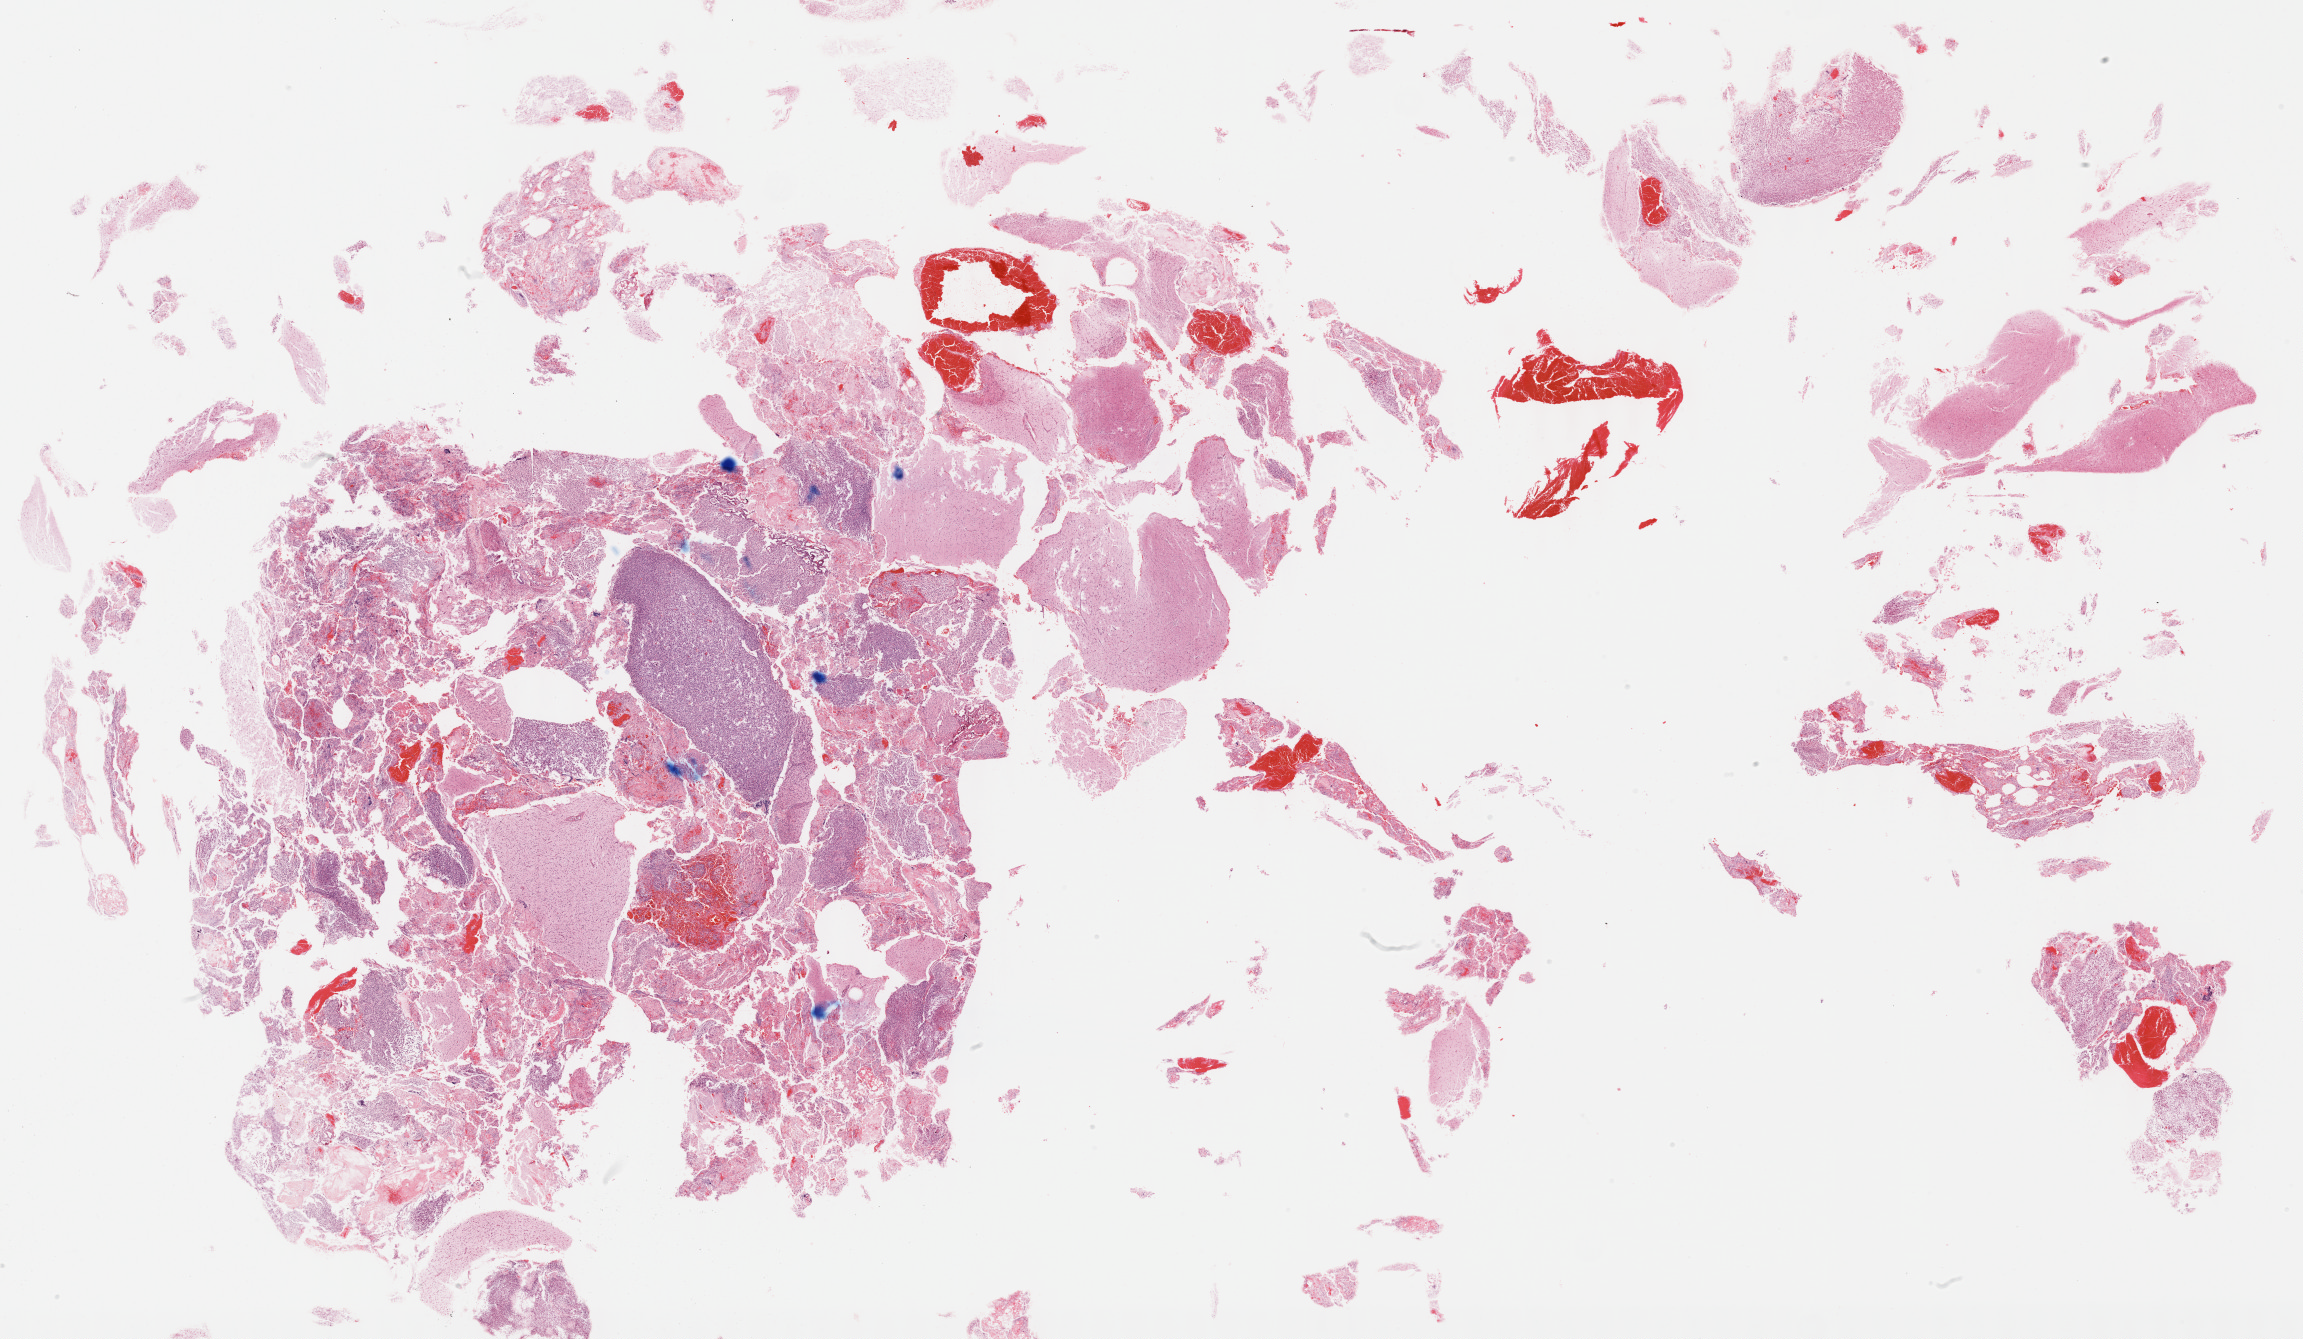
Digitized Hematoxylin and eosin (H&E) stained tissue section (whole slide), a low-resolution overview of the entire scanned area, about 37.2 x 21.6 mm. Formalin-fixed paraffin-embedded (FFPE) diagnostic section. Sample: primary tumour, brain. Female patient; age at initial diagnosis 59 years.
Diagnosis: Glioblastoma.